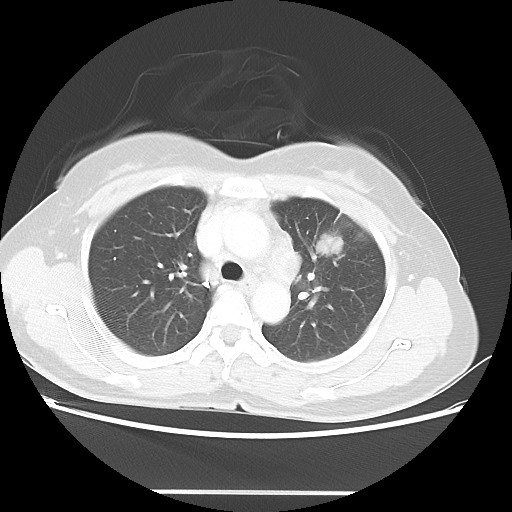
Chest CT, one axial slice. Position 33 of 46 along the scan axis. 100 kVp. Lung window (W 1500 / L -600 HU). 5 mm slice thickness. 512 × 512 image matrix, field of view 360 × 360 mm. Female patient, age 50 years. Case-level facts recorded for this patient, not image findings: clinical TNM (as recorded): T1c N1 M0.
Outlined on this slice (rectangle marked by the reading radiologist):
- lung tumour (recorded histology: adenocarcinoma): bounding box [x1, y1, x2, y2] px = [314, 233, 346, 255]